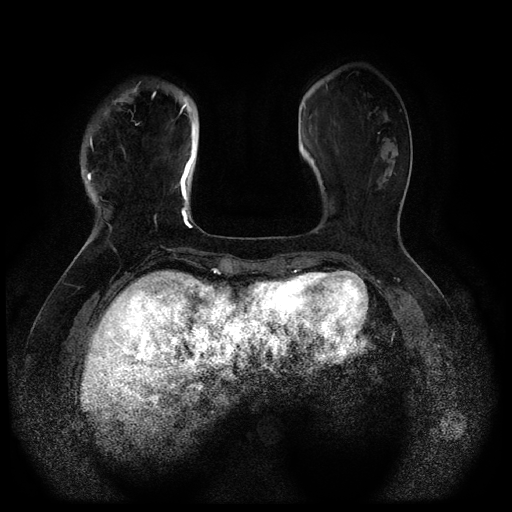
Breast MRI (dynamic contrast-enhanced, multi-phase), one axial slice; position 27 of 116 along the scan axis; dynamic contrast-enhanced series, time point 2 of 5 at this slice position (early post-contrast); 1.5 T; TE 2.6 ms, TR 5.3 ms; 2 mm slice thickness; 512 × 512 image matrix, field of view 350 × 350 mm. Patient: female, 51 years.
Structures marked on this image (semi-automatic segmentation, software-assisted and operator-edited):
- breast lesion (labelled 'tumour' in the annotation; benign lesions carry a separate 'benign' label): bounding box <112,86,138,111> (left, top, right, bottom; pixels)